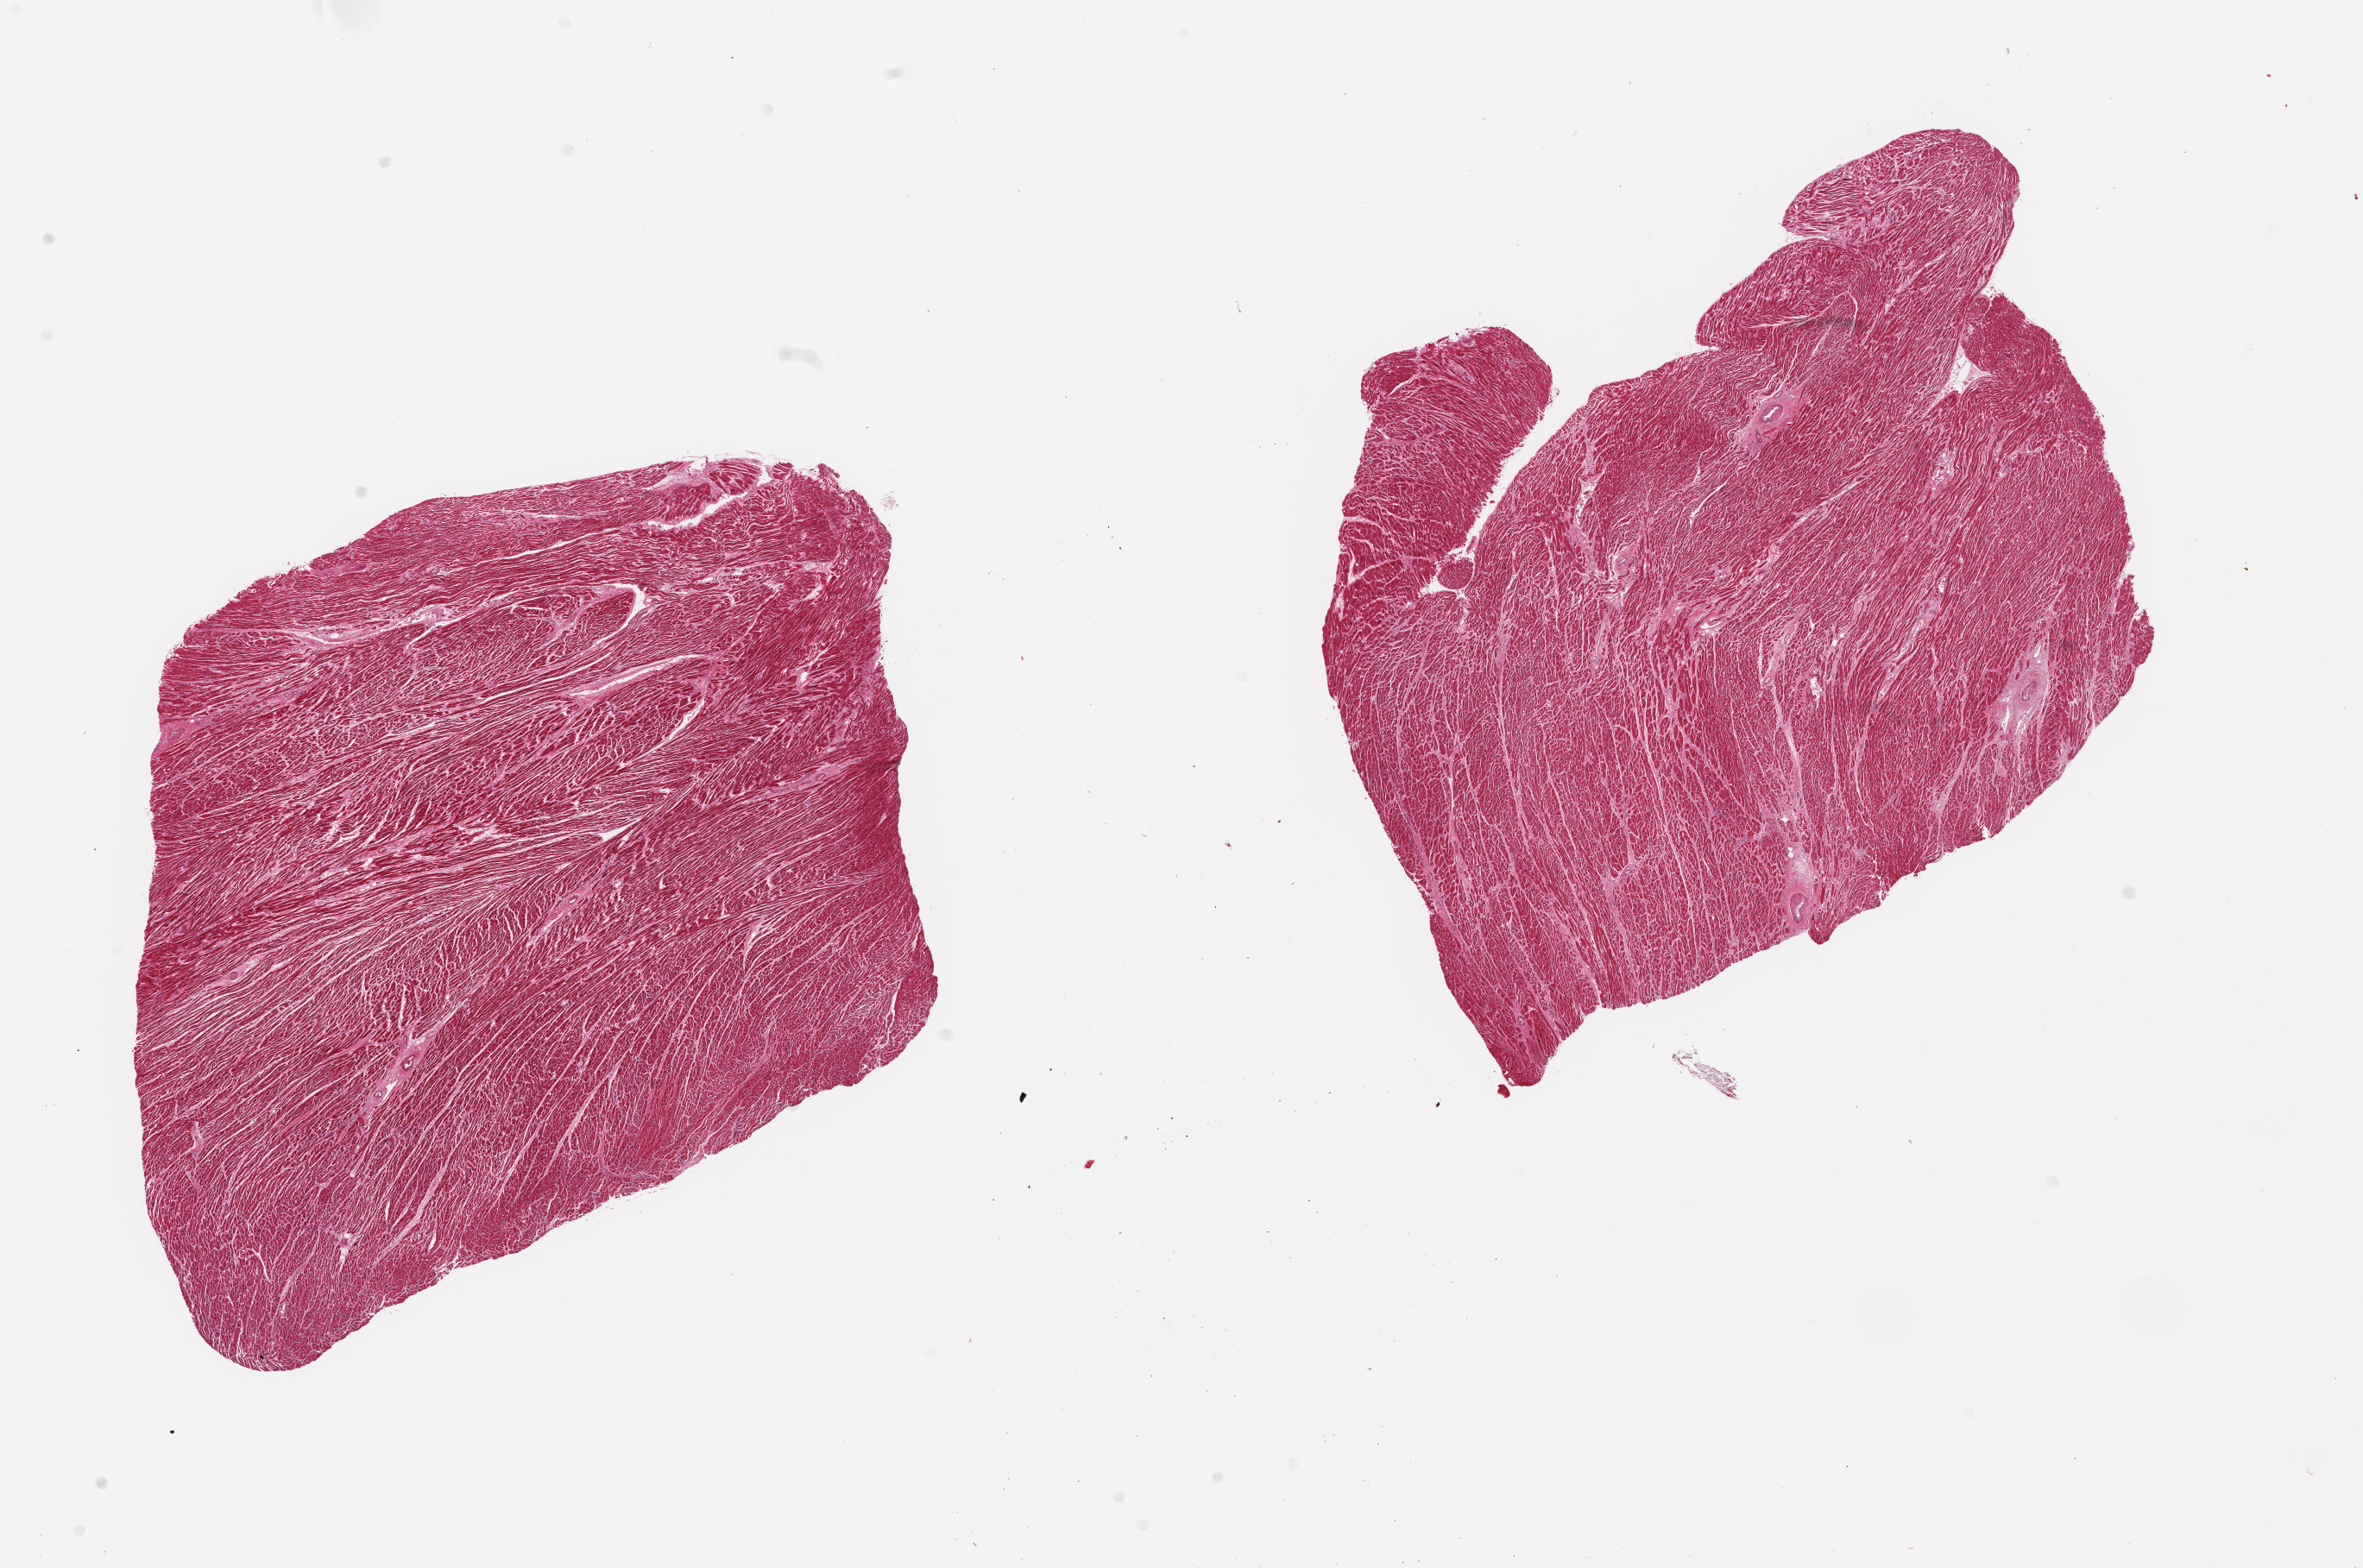
Whole-slide image, H&E stain — whole scanned area (about 21.7 x 14.4 mm, from a 20x scan) shown as a low-resolution overview. PAXgene-fixed, paraffin-embedded tissue. Sampled site (target tissue): heart. Tissue donor sample. Donor: female.
• pathologist's review note for this sample: 2 pieces; mild patchy scarring